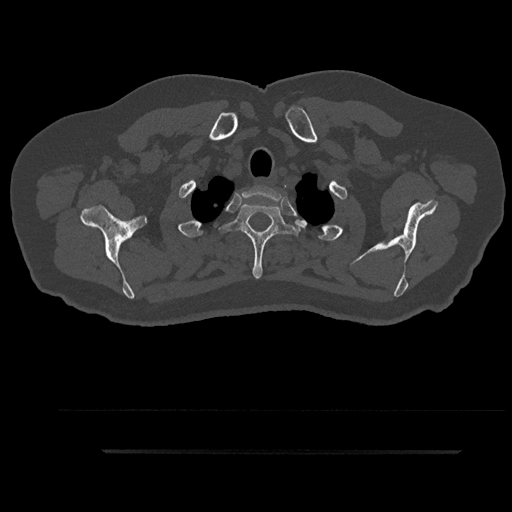
CT including the spine, one axial slice. Bone window (W 1800 / L 400 HU). 0.5 mm slice thickness. 512 × 512 image matrix. Patient: male, 63 years. From the clinical record (not read from this slice): primary cancer: renal.
Outlined on this slice (semi-automatic segmentation, software-assisted and operator-edited):
- T1 vertebra: bounding box [x1, y1, x2, y2] px = [238, 186, 284, 217]
- T2 vertebra: [222, 203, 304, 279]